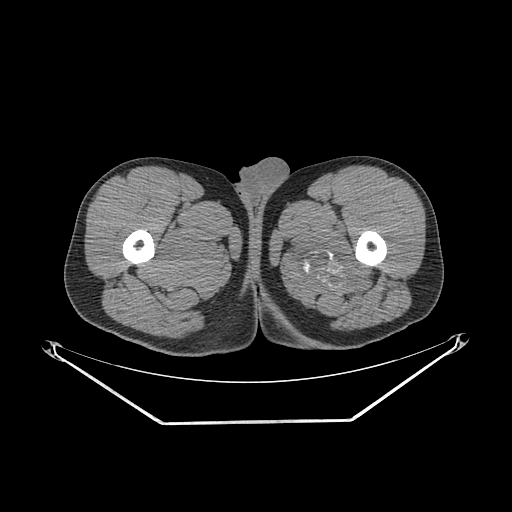
CT of an extremity soft-tissue mass (from a PET/CT study), one axial slice. Position 257 of 267 along the scan axis. Reconstruction kernel SOFT. 140 kVp. Soft-tissue window (W 400 / L 40 HU). 3.75 mm slice thickness. 512 × 512 image matrix. Male patient. From the clinical record (not read from this slice): histological type: extraskeletal osteosarcoma; grade: high; site of the primary tumour: left adductur.
Outlined on this slice (expert contour drawn on MRI and transferred to this co-registered scan by the dataset authors):
- gross tumour volume (mass): bounding box [x1, y1, x2, y2] px = [290, 210, 378, 300]